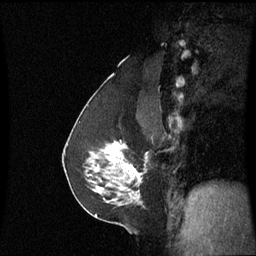
Breast MRI (dynamic contrast-enhanced), one sagittal slice; position 37 of 60 along the scan axis; dynamic contrast-enhanced series, image 2 of 3 at this slice position (ordered by acquisition); 1.5 T; TE 4.2 ms, TR 8.9 ms; 256 × 256 image matrix. Patient: female, 58 years. From the clinical record (not read from this slice): setting: breast cancer imaged before/during neoadjuvant chemotherapy; receptor status: triple-negative.
Outlined on this slice (semi-automatically segmented with operator editing):
- analysis volume of interest (the breast-tissue region the enhancement analysis was run in; not a lesion): bounding box <90,140,149,193> (left, top, right, bottom; pixels)
- tumour enhancement mask (voxels above the 70 % enhancement threshold inside the analysis volume of interest): <106,142,137,175>